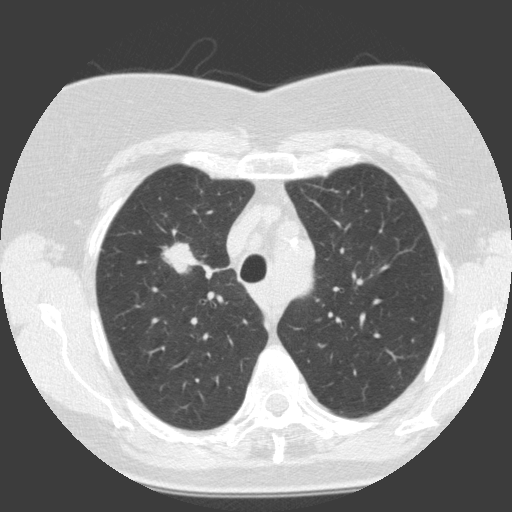
Low-dose screening chest CT, one axial slice. Slice 108 of 146 in the series (ordered by position). 120 kVp. Lung window (W 1500 / L -600 HU). 2 mm slice thickness. 512 × 512 image matrix.
Outlined on this slice (manually delineated by an expert):
- lesion 1 (tumor, upper lobe of right lung): box from (x=162, y=242) to (x=196, y=274) px